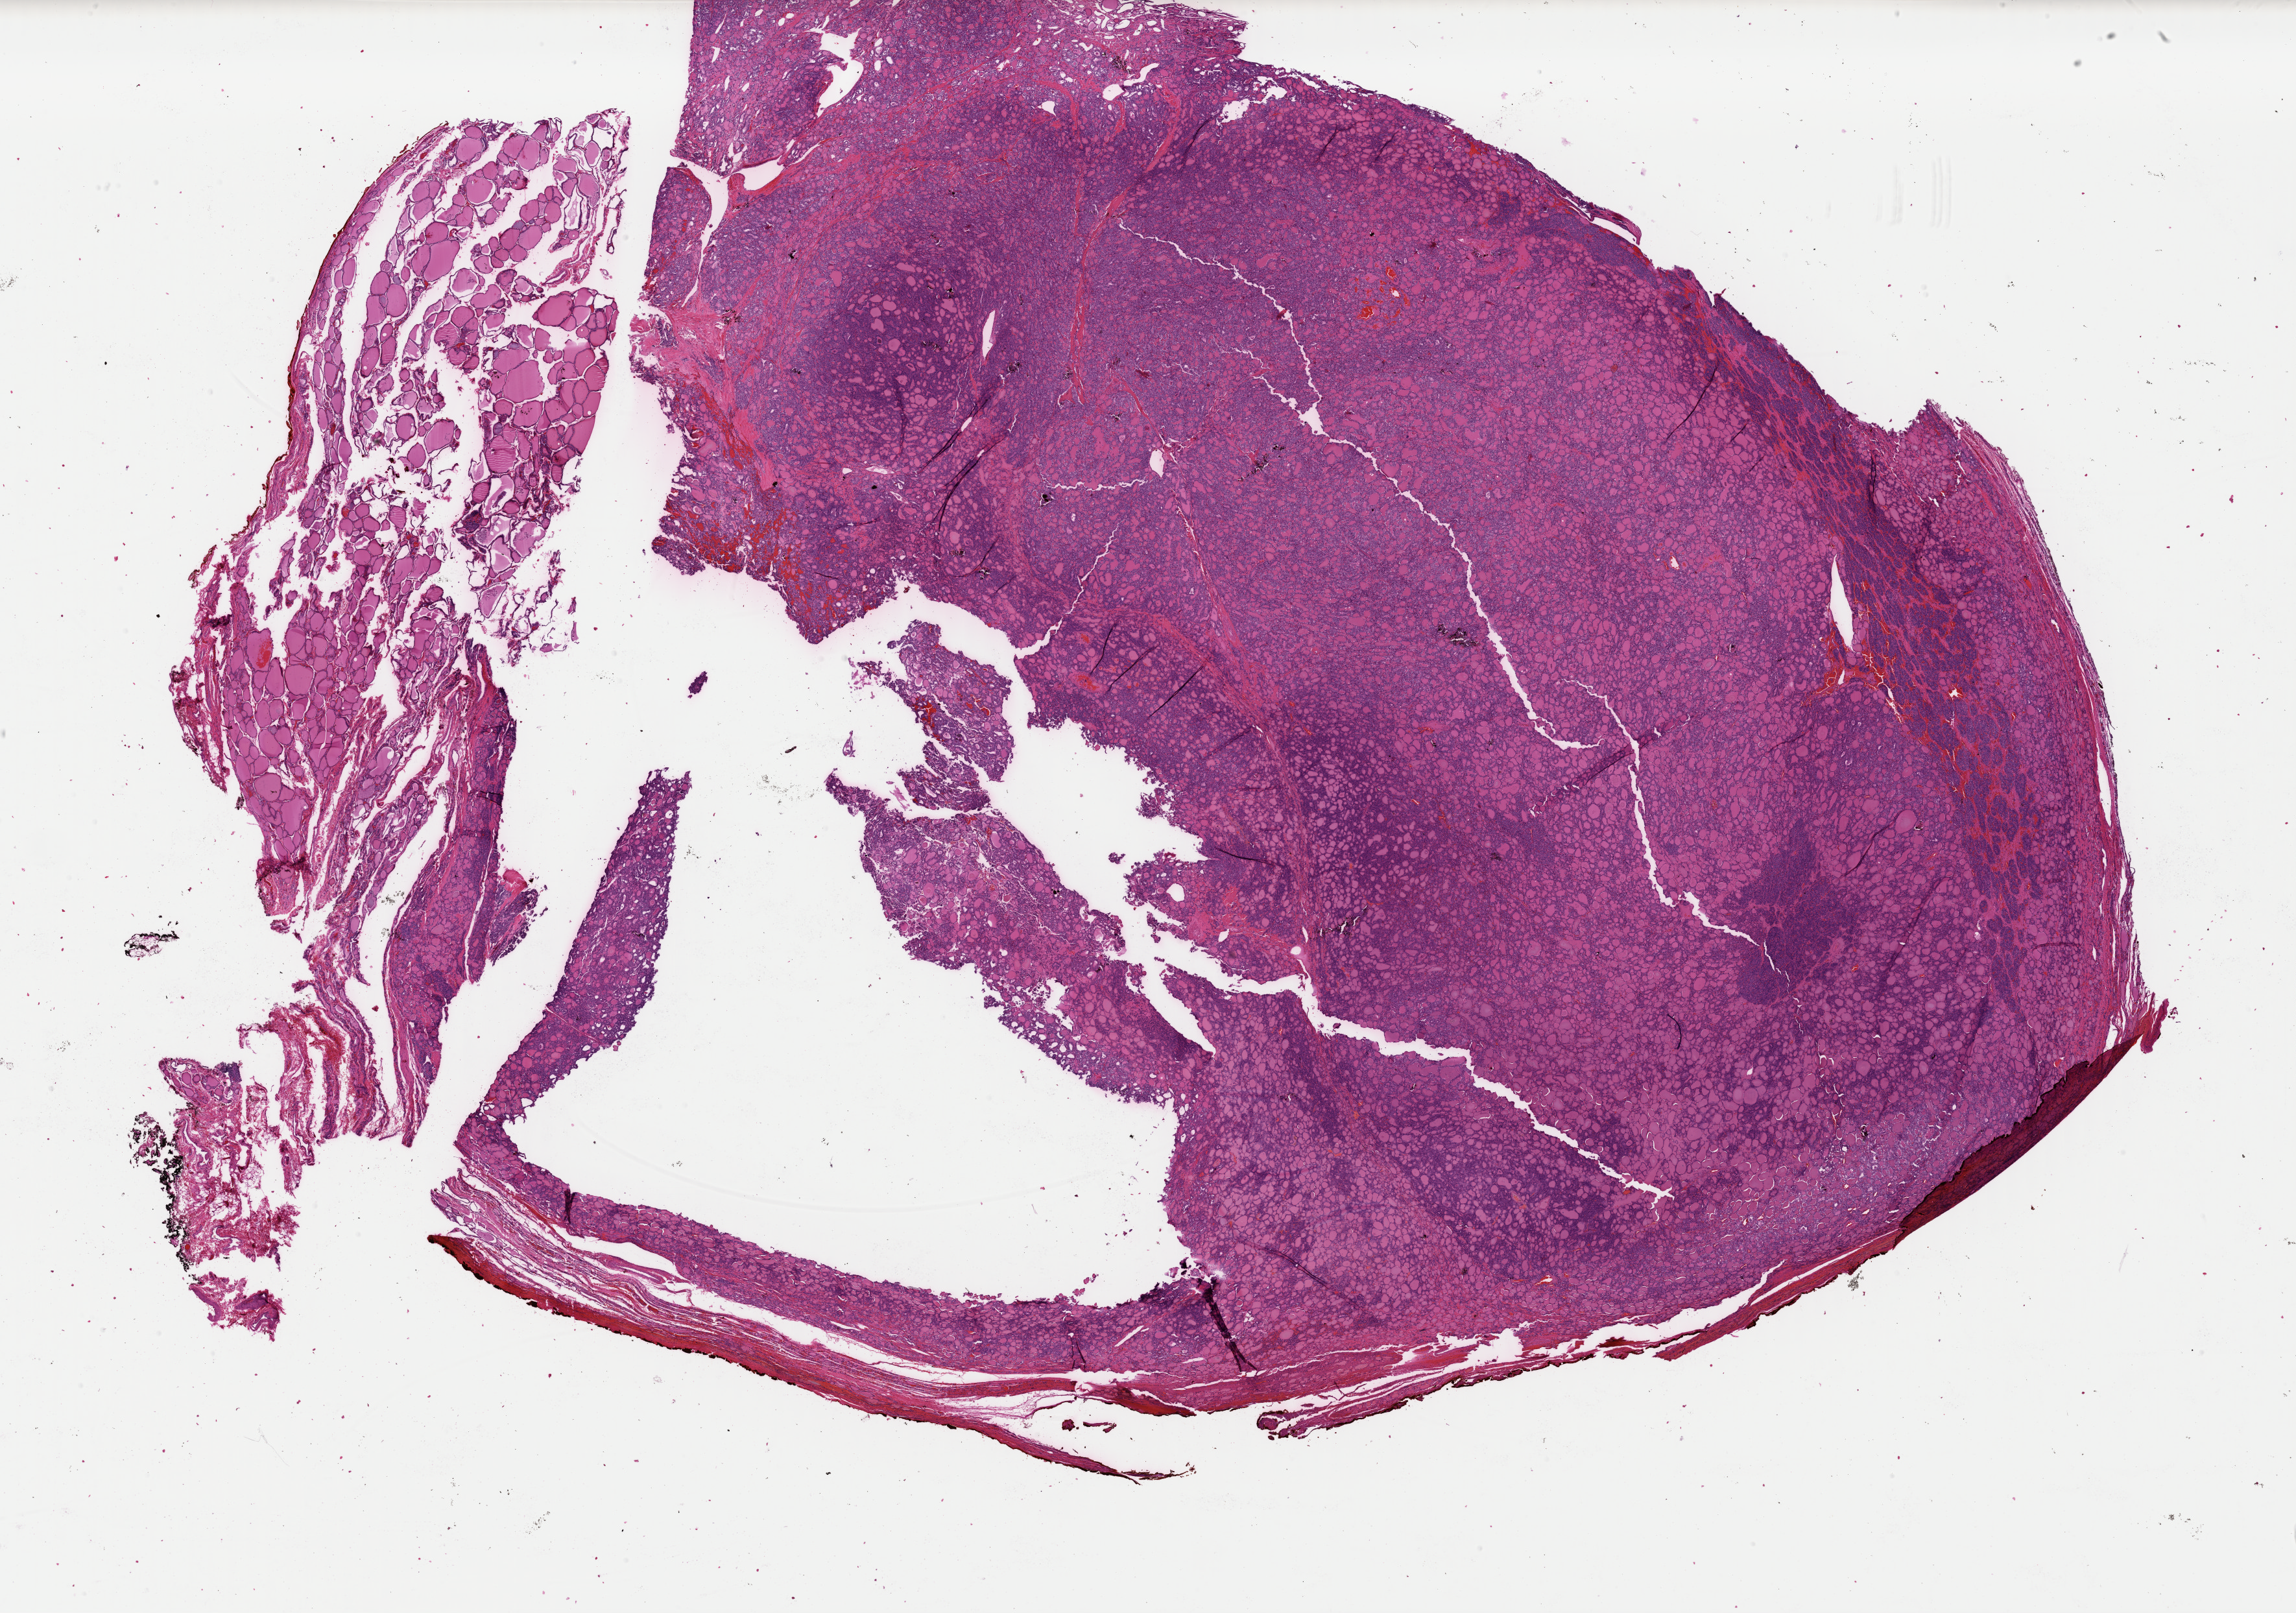
Whole-slide histology image, H&E, a low-resolution overview of the entire scanned area, about 28.0 x 19.6 mm; formalin-fixed paraffin-embedded (FFPE) diagnostic section; thyroid, primary tumour sample. Female patient; age at initial diagnosis 32 years.
* diagnosis: Papillary carcinoma, follicular variant
* lymph nodes positive (case pathology): 0 of 1 examined
* AJCC pathologic stage: I (7th edition)